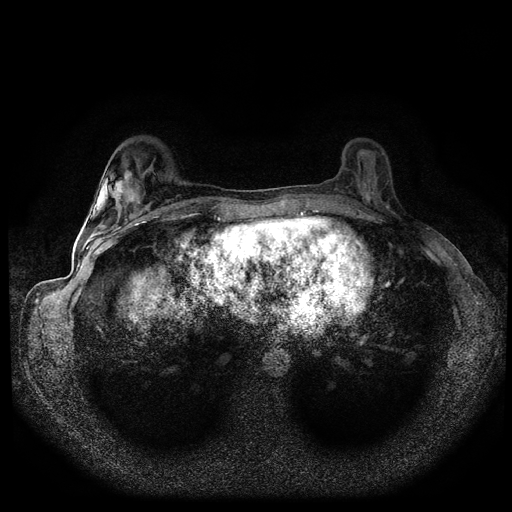
Breast MRI (dynamic contrast-enhanced, multi-phase), one axial slice. Slice 33 of 108 in the series (ordered by position). Dynamic contrast-enhanced series, time point 2 of 5 at this slice position (early post-contrast). 1.5 T. TE 2.7 ms, TR 5.5 ms. 2 mm slice thickness. 512 × 512 image matrix. Patient: female, 36 years.
Outlined on this slice (semi-automatic segmentation, software-assisted and operator-edited):
- breast lesion (labelled benign in the annotation): bounding box <106,169,136,205> (left, top, right, bottom; pixels)